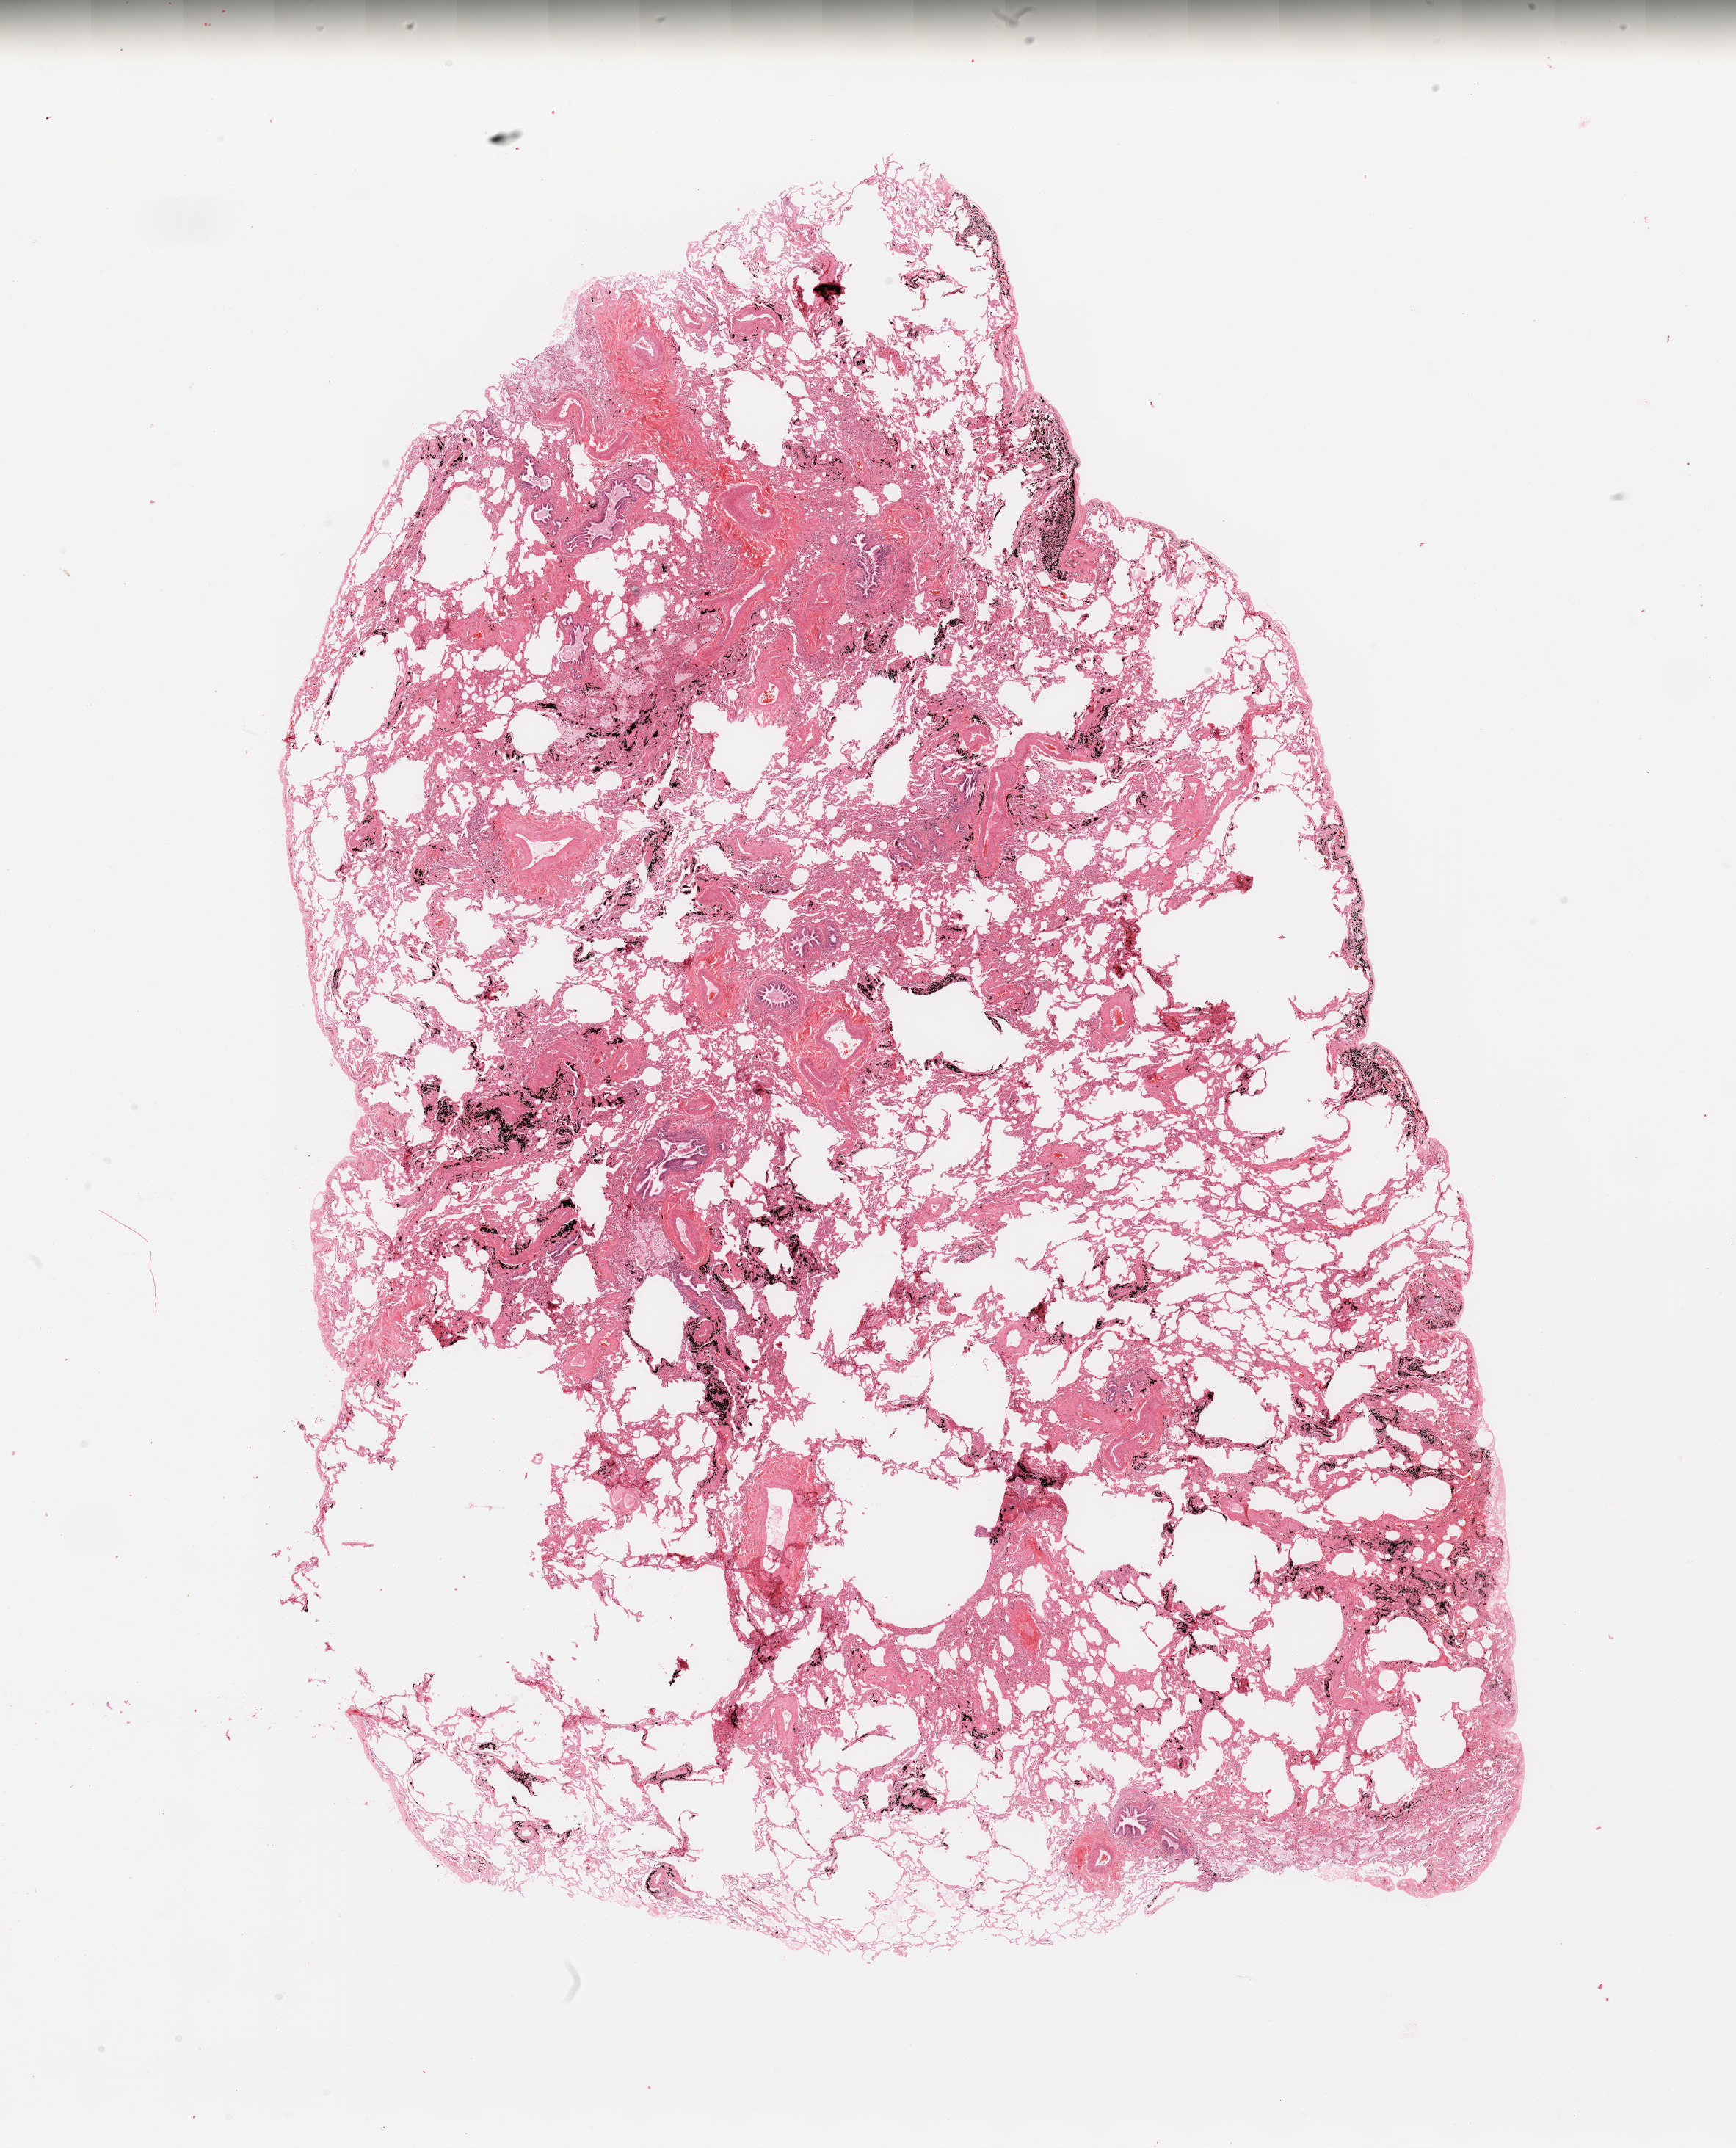
Hematoxylin and eosin (H&E) stained whole-slide image — low-resolution overview of the scanned area, about 18.7 x 23.1 mm, lung, normal (non-tumour) tissue. Patient: male, age 64 years.
This section: normal (non-tumour) tissue from the same patient. Patient diagnosis: Squamous cell carcinoma, NOS.